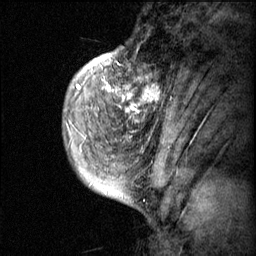
Breast MRI (dynamic contrast-enhanced), one sagittal slice; slice 12 of 60 in the series (ordered by position); dynamic contrast-enhanced series, image 2 of 3 at this slice position (ordered by acquisition); 1.5 T; TE 4.2 ms, TR 11.1 ms; 2 mm slice thickness; 256 × 256 image matrix, field of view 180 × 180 mm. Patient: female, 50 years.
Structures marked on this image (semi-automatic segmentation, software-assisted and operator-edited):
- analysis volume of interest (the breast-tissue region the enhancement analysis was run in; not a lesion): bounding box [x1, y1, x2, y2] px = [82, 56, 168, 143]
- tumour enhancement mask (voxels above the 70 % enhancement threshold inside the analysis volume of interest): [83, 56, 167, 143]